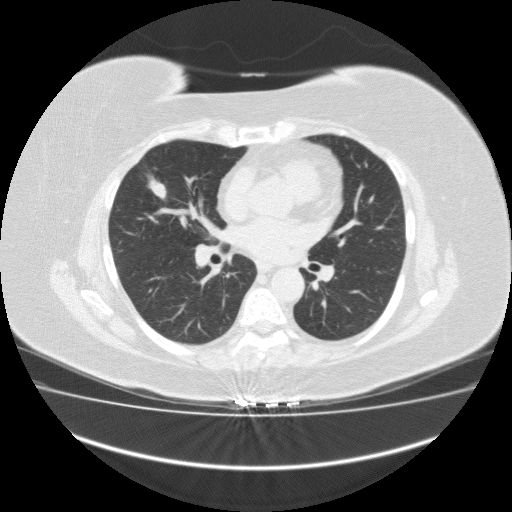
Low-dose screening chest CT, one axial slice. Position 87 of 162 along the scan axis. 120 kVp. Lung window (W 1500 / L -600 HU). 2 mm slice thickness. 512 × 512 image matrix, field of view 420 × 420 mm.
Structures marked on this image (manually delineated by an expert):
- lesion 1 (tumor, middle lobe of right lung): bounding box [x1, y1, x2, y2] px = [147, 178, 167, 200]